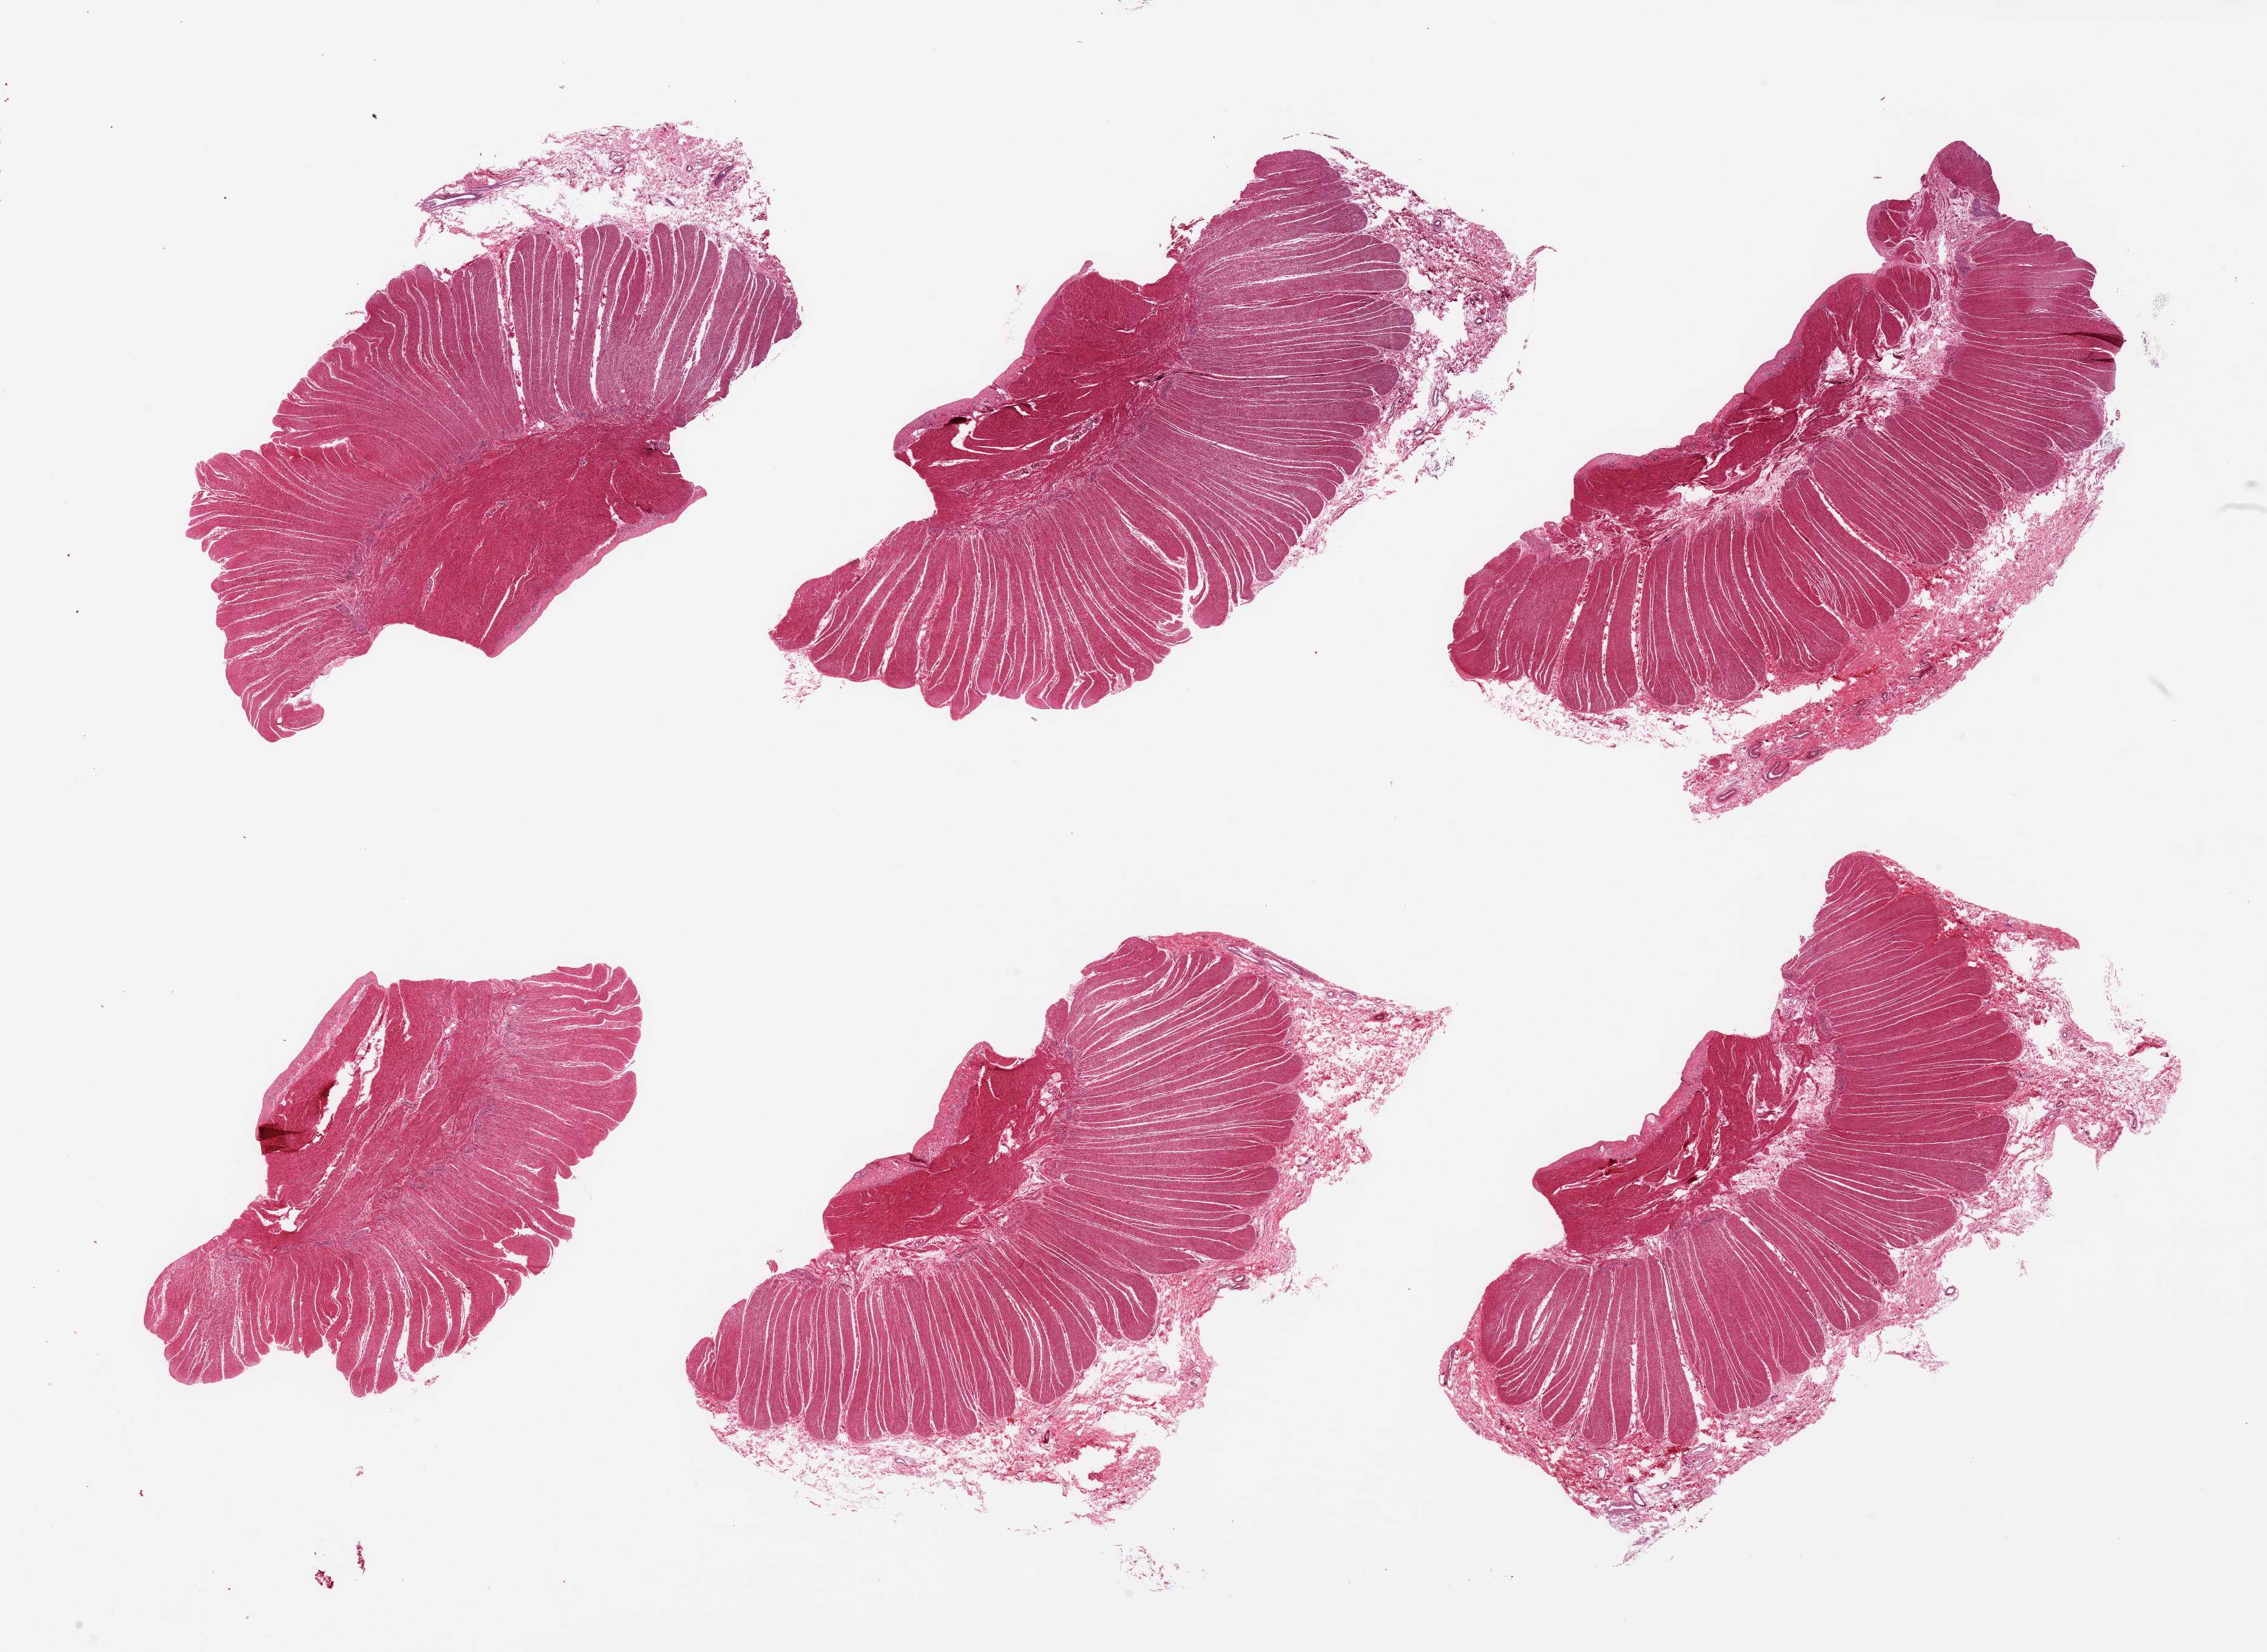
Digitized hematoxylin and eosin (H&E)-stained section, low-resolution overview of the scanned area, about 29.5 x 21.5 mm, PAXgene-fixed, paraffin-embedded tissue, section of sigmoid colon (target tissue), donor tissue sample. Donor: male.
Pathologist's review note for this sample: 6 pieces; well dissected muscularis propria with up to 10% submucosal stroma.